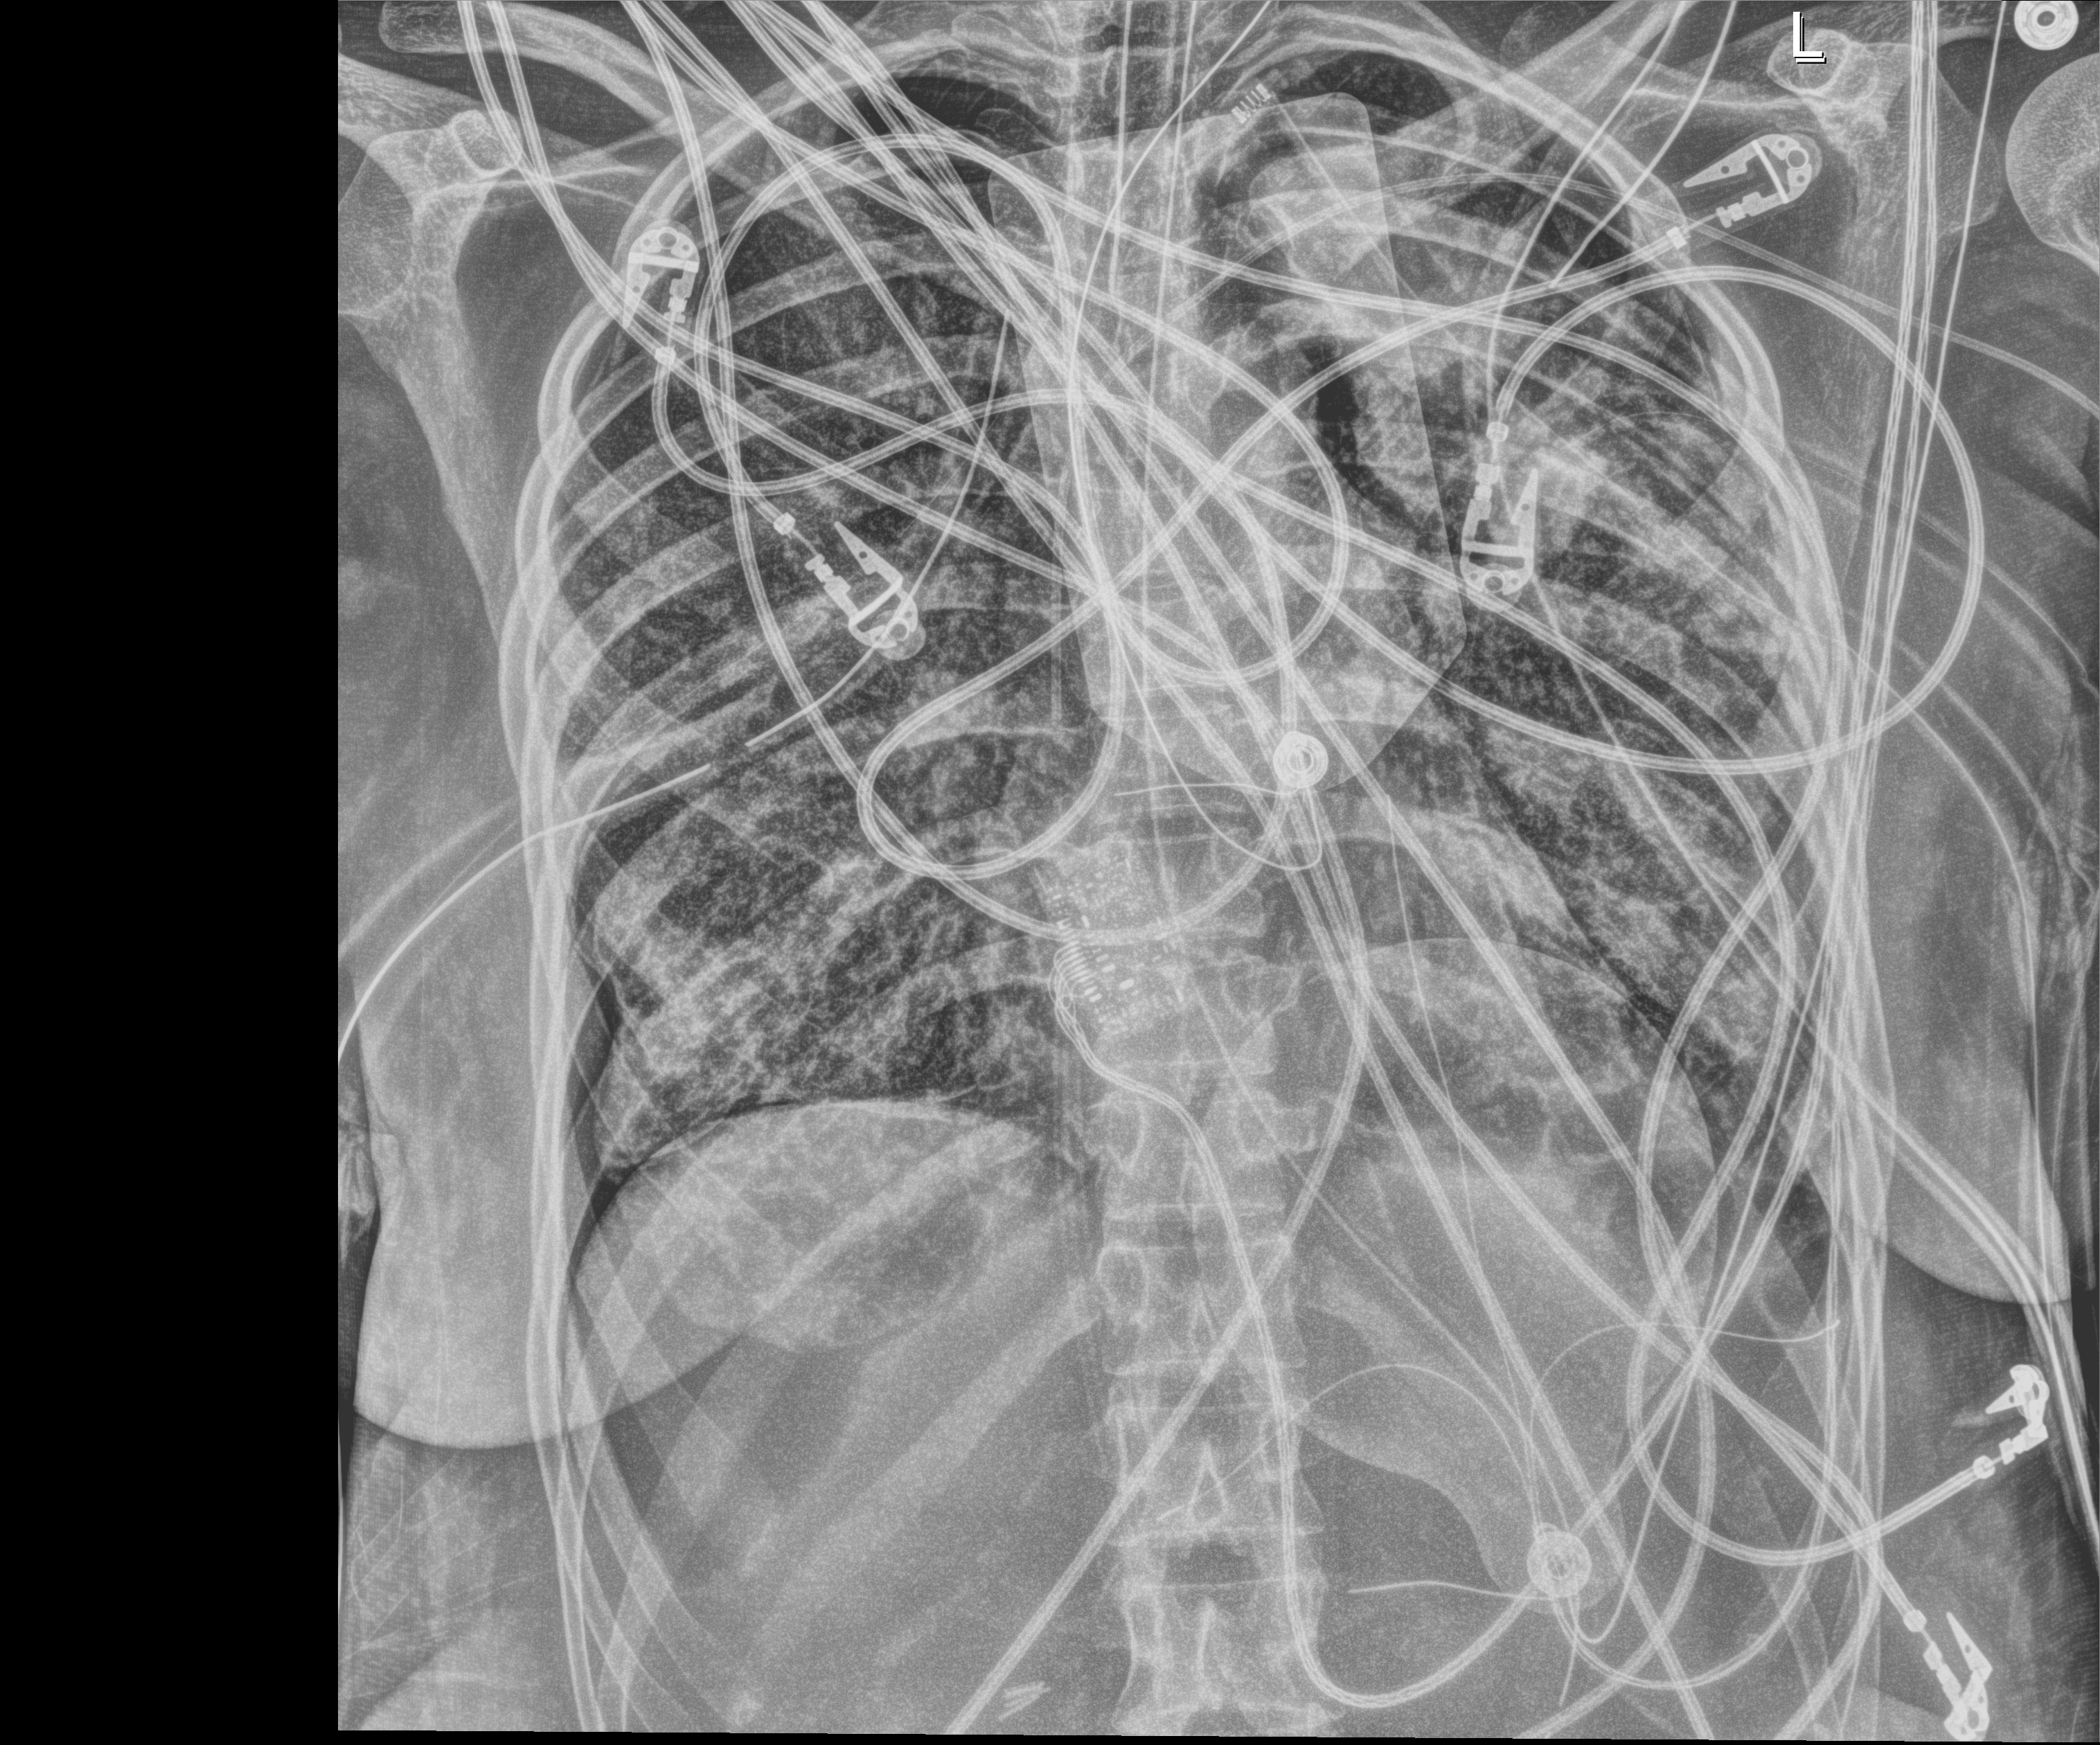
Portable chest radiograph; anteroposterior (AP) projection. Adult patient hospitalised with COVID-19, age 18–59 years.
Hospital-stay facts (about this admission, not read from this image; timing relative to this image not recorded):
- admitted to intensive care during this hospital stay: yes
- length of hospital stay: 30 days